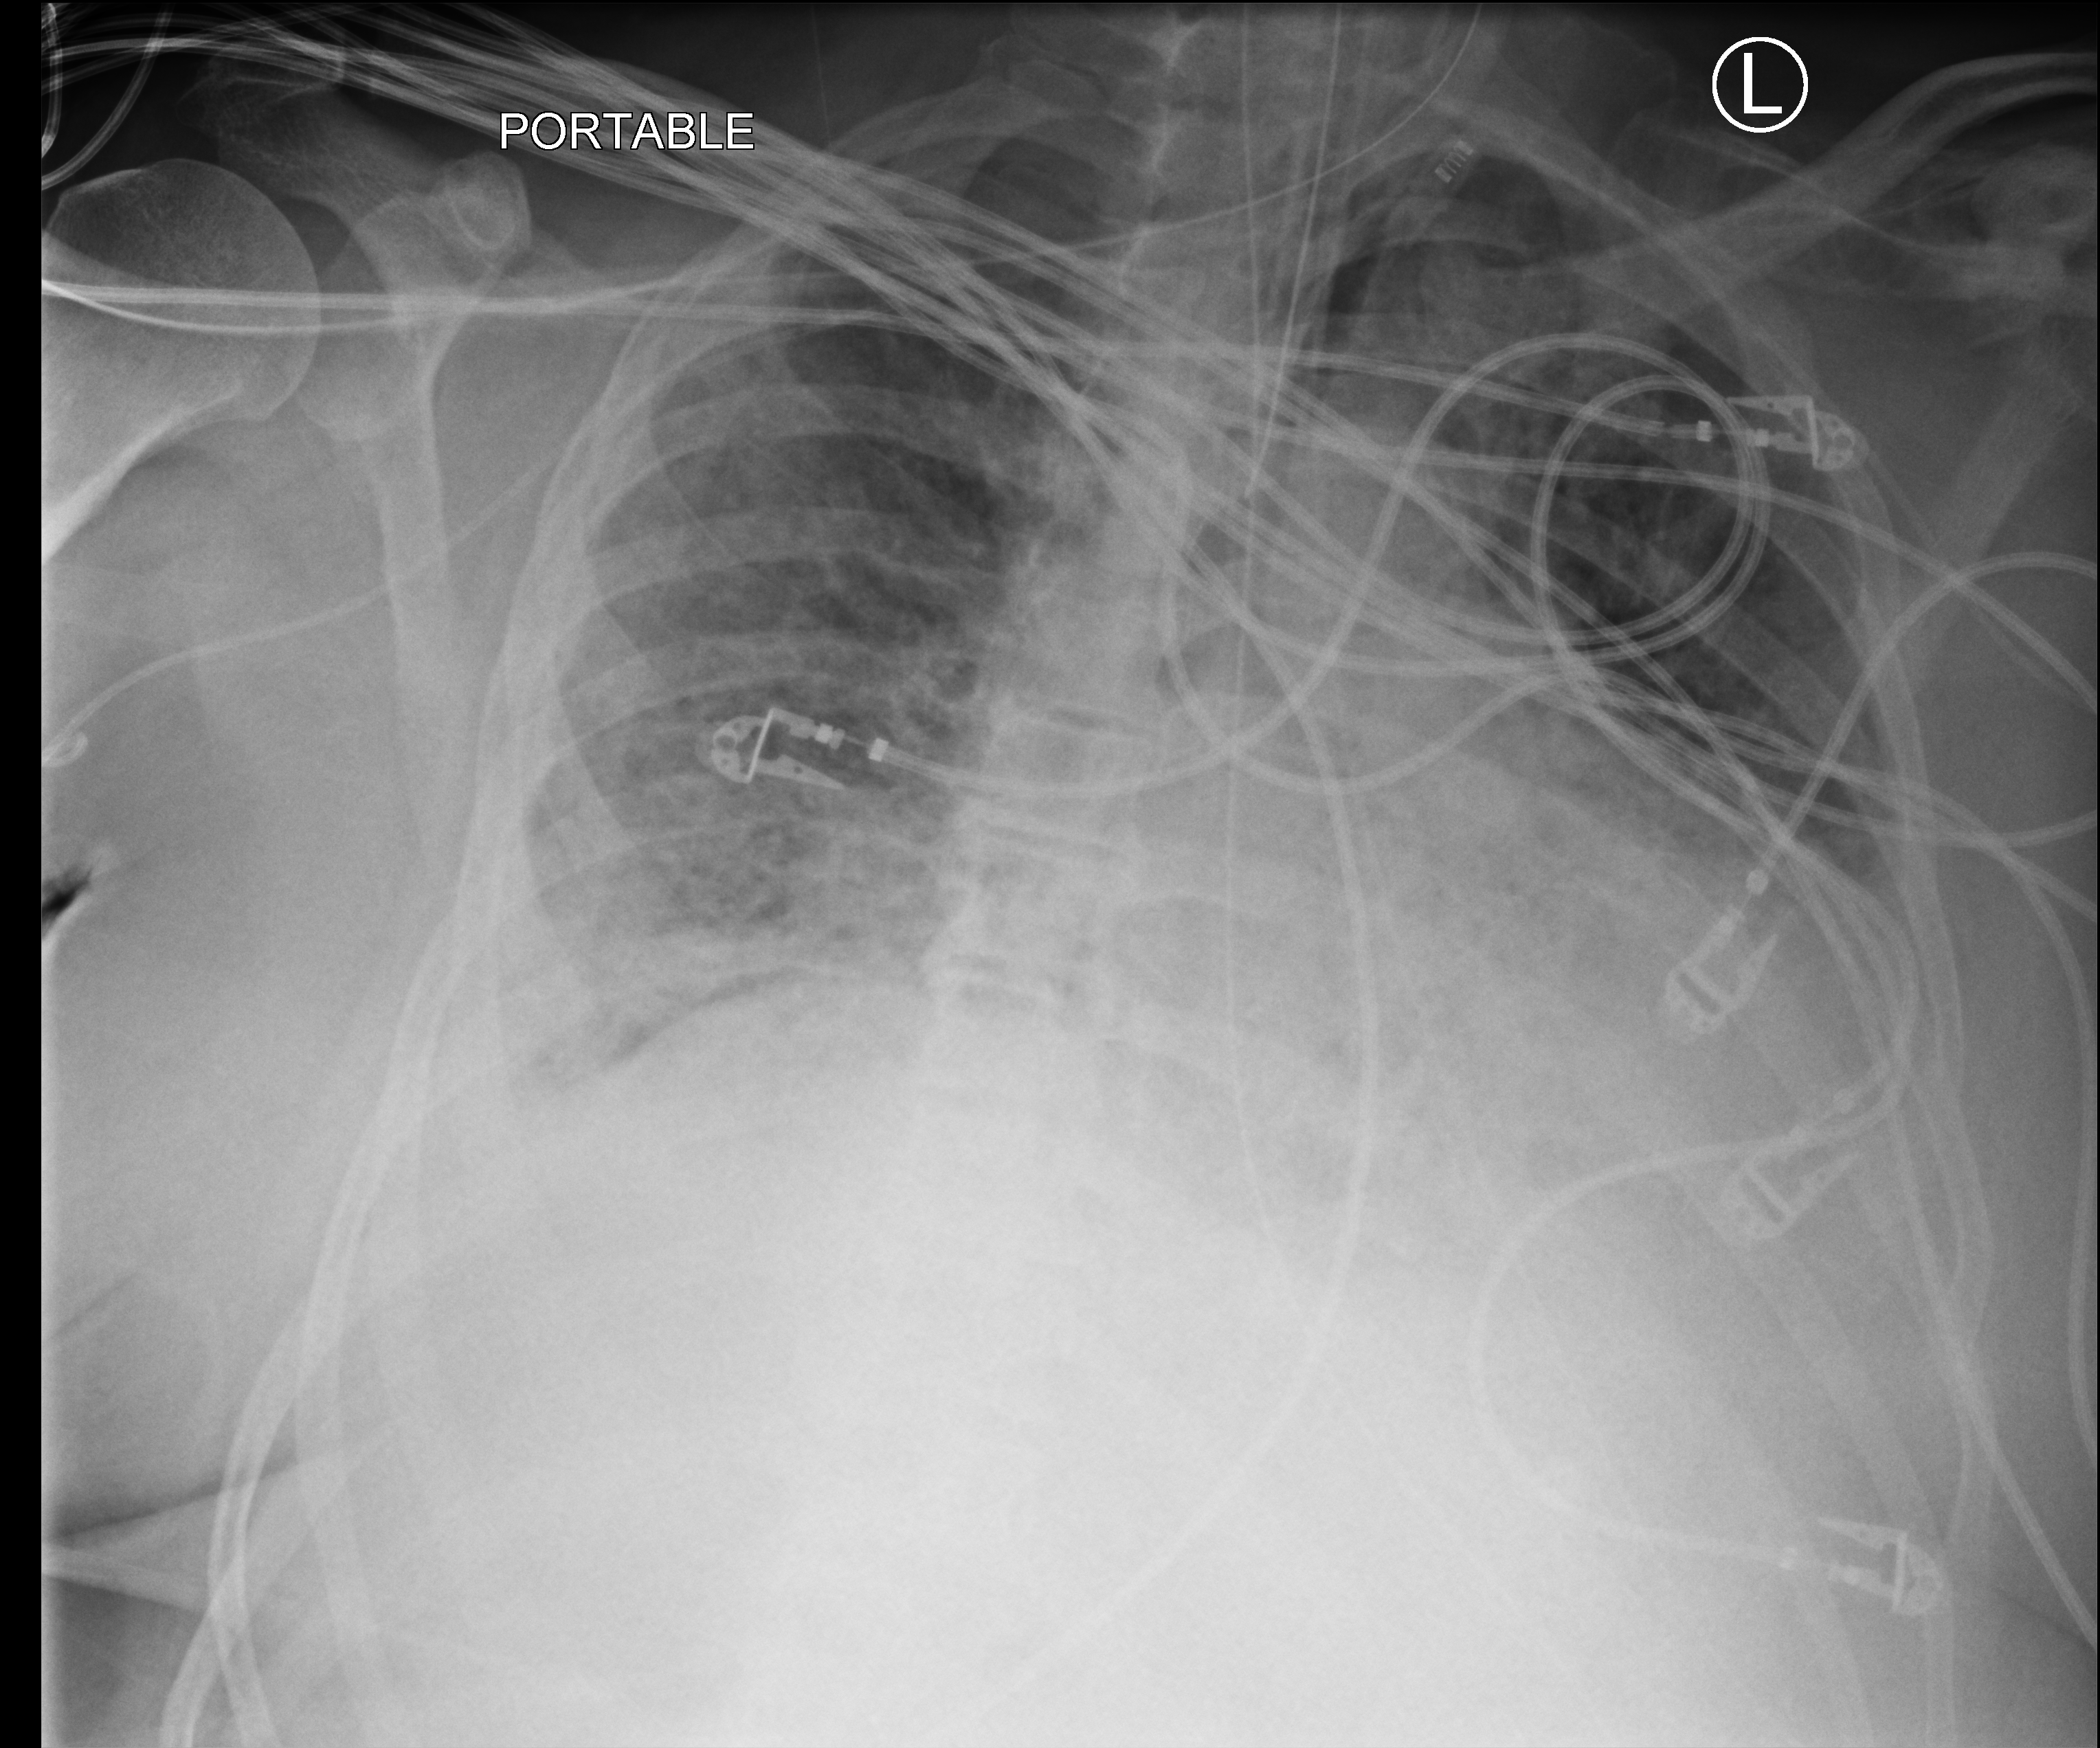
Bedside chest radiograph (computed radiography), anteroposterior (AP) projection. Patient hospitalised with COVID-19; male, aged 60–74 years.
Hospital-stay facts (about this admission, not read from this image; timing relative to this image not recorded):
- admitted to intensive care during this hospital stay: yes
- smoking status (admission record): former
- mechanically ventilated during this hospital stay: yes